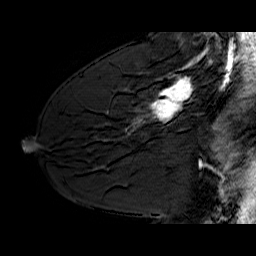
Breast MRI (dynamic contrast-enhanced), one sagittal slice. Position 39 of 60 along the scan axis. Dynamic contrast-enhanced series, time point 2 of 6 at this slice position (early post-contrast). 1.5 T. TE 6.4 ms, TR 32.9 ms. 256 × 256 image matrix, field of view 200 × 200 mm. Female patient. From the clinical record (not read from this slice): setting: breast cancer imaged before/during neoadjuvant chemotherapy; receptor status: HER2-positive.
Outlined on this slice (semi-automatically segmented with operator editing):
- analysis volume of interest (the breast-tissue region the enhancement analysis was run in; not a lesion): bounding box <130,62,210,128> (left, top, right, bottom; pixels)
- tumour enhancement mask (voxels above the 100 % enhancement threshold inside the analysis volume of interest): <149,62,196,121>